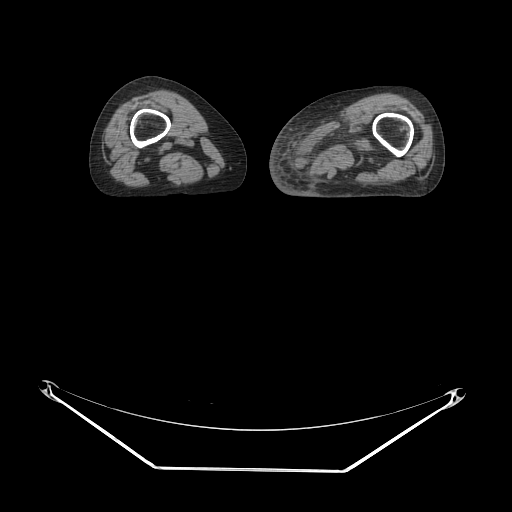
CT of an extremity soft-tissue mass (from a PET/CT study), one axial slice. Position 7 of 91 along the scan axis. 140 kVp. Soft-tissue window (W 400 / L 40 HU). 512 × 512 image matrix. Female patient. From the clinical record (not read from this slice): histological type: pleomorphic leiomyosarcoma; grade: high; site of the primary tumour: left thigh.
Structures marked on this image (expert contour drawn on MRI and transferred to this co-registered scan by the dataset authors):
- gross tumour volume including surrounding oedema: bounding box [x1, y1, x2, y2] px = [302, 112, 382, 175]